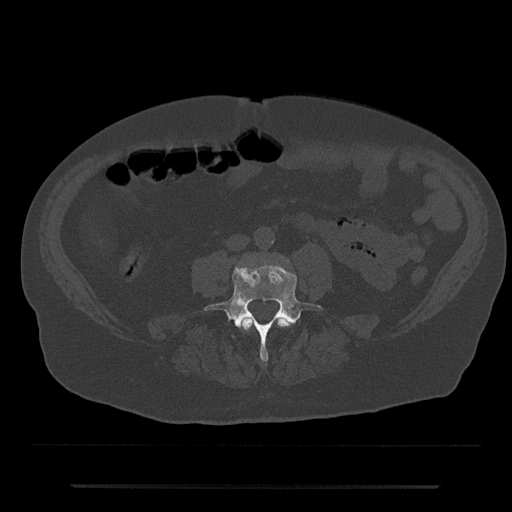
CT including the spine, one axial slice; slice 361 of 797 in the series (ordered by position); bone window (W 1800 / L 400 HU); 0.5 mm slice thickness; 512 × 512 image matrix, field of view 434 × 434 mm. Male patient, age 80 years. From the clinical record (not read from this slice): primary cancer: prostate; vertebrae with lytic lesions (as recorded): L1, T11.
Annotated regions visible in this slice (semi-automatic segmentation, software-assisted and operator-edited):
- L3 vertebra: bounding box (x1, y1, x2, y2) in pixels: (240, 317, 291, 331)
- L4 vertebra: (205, 263, 322, 361)